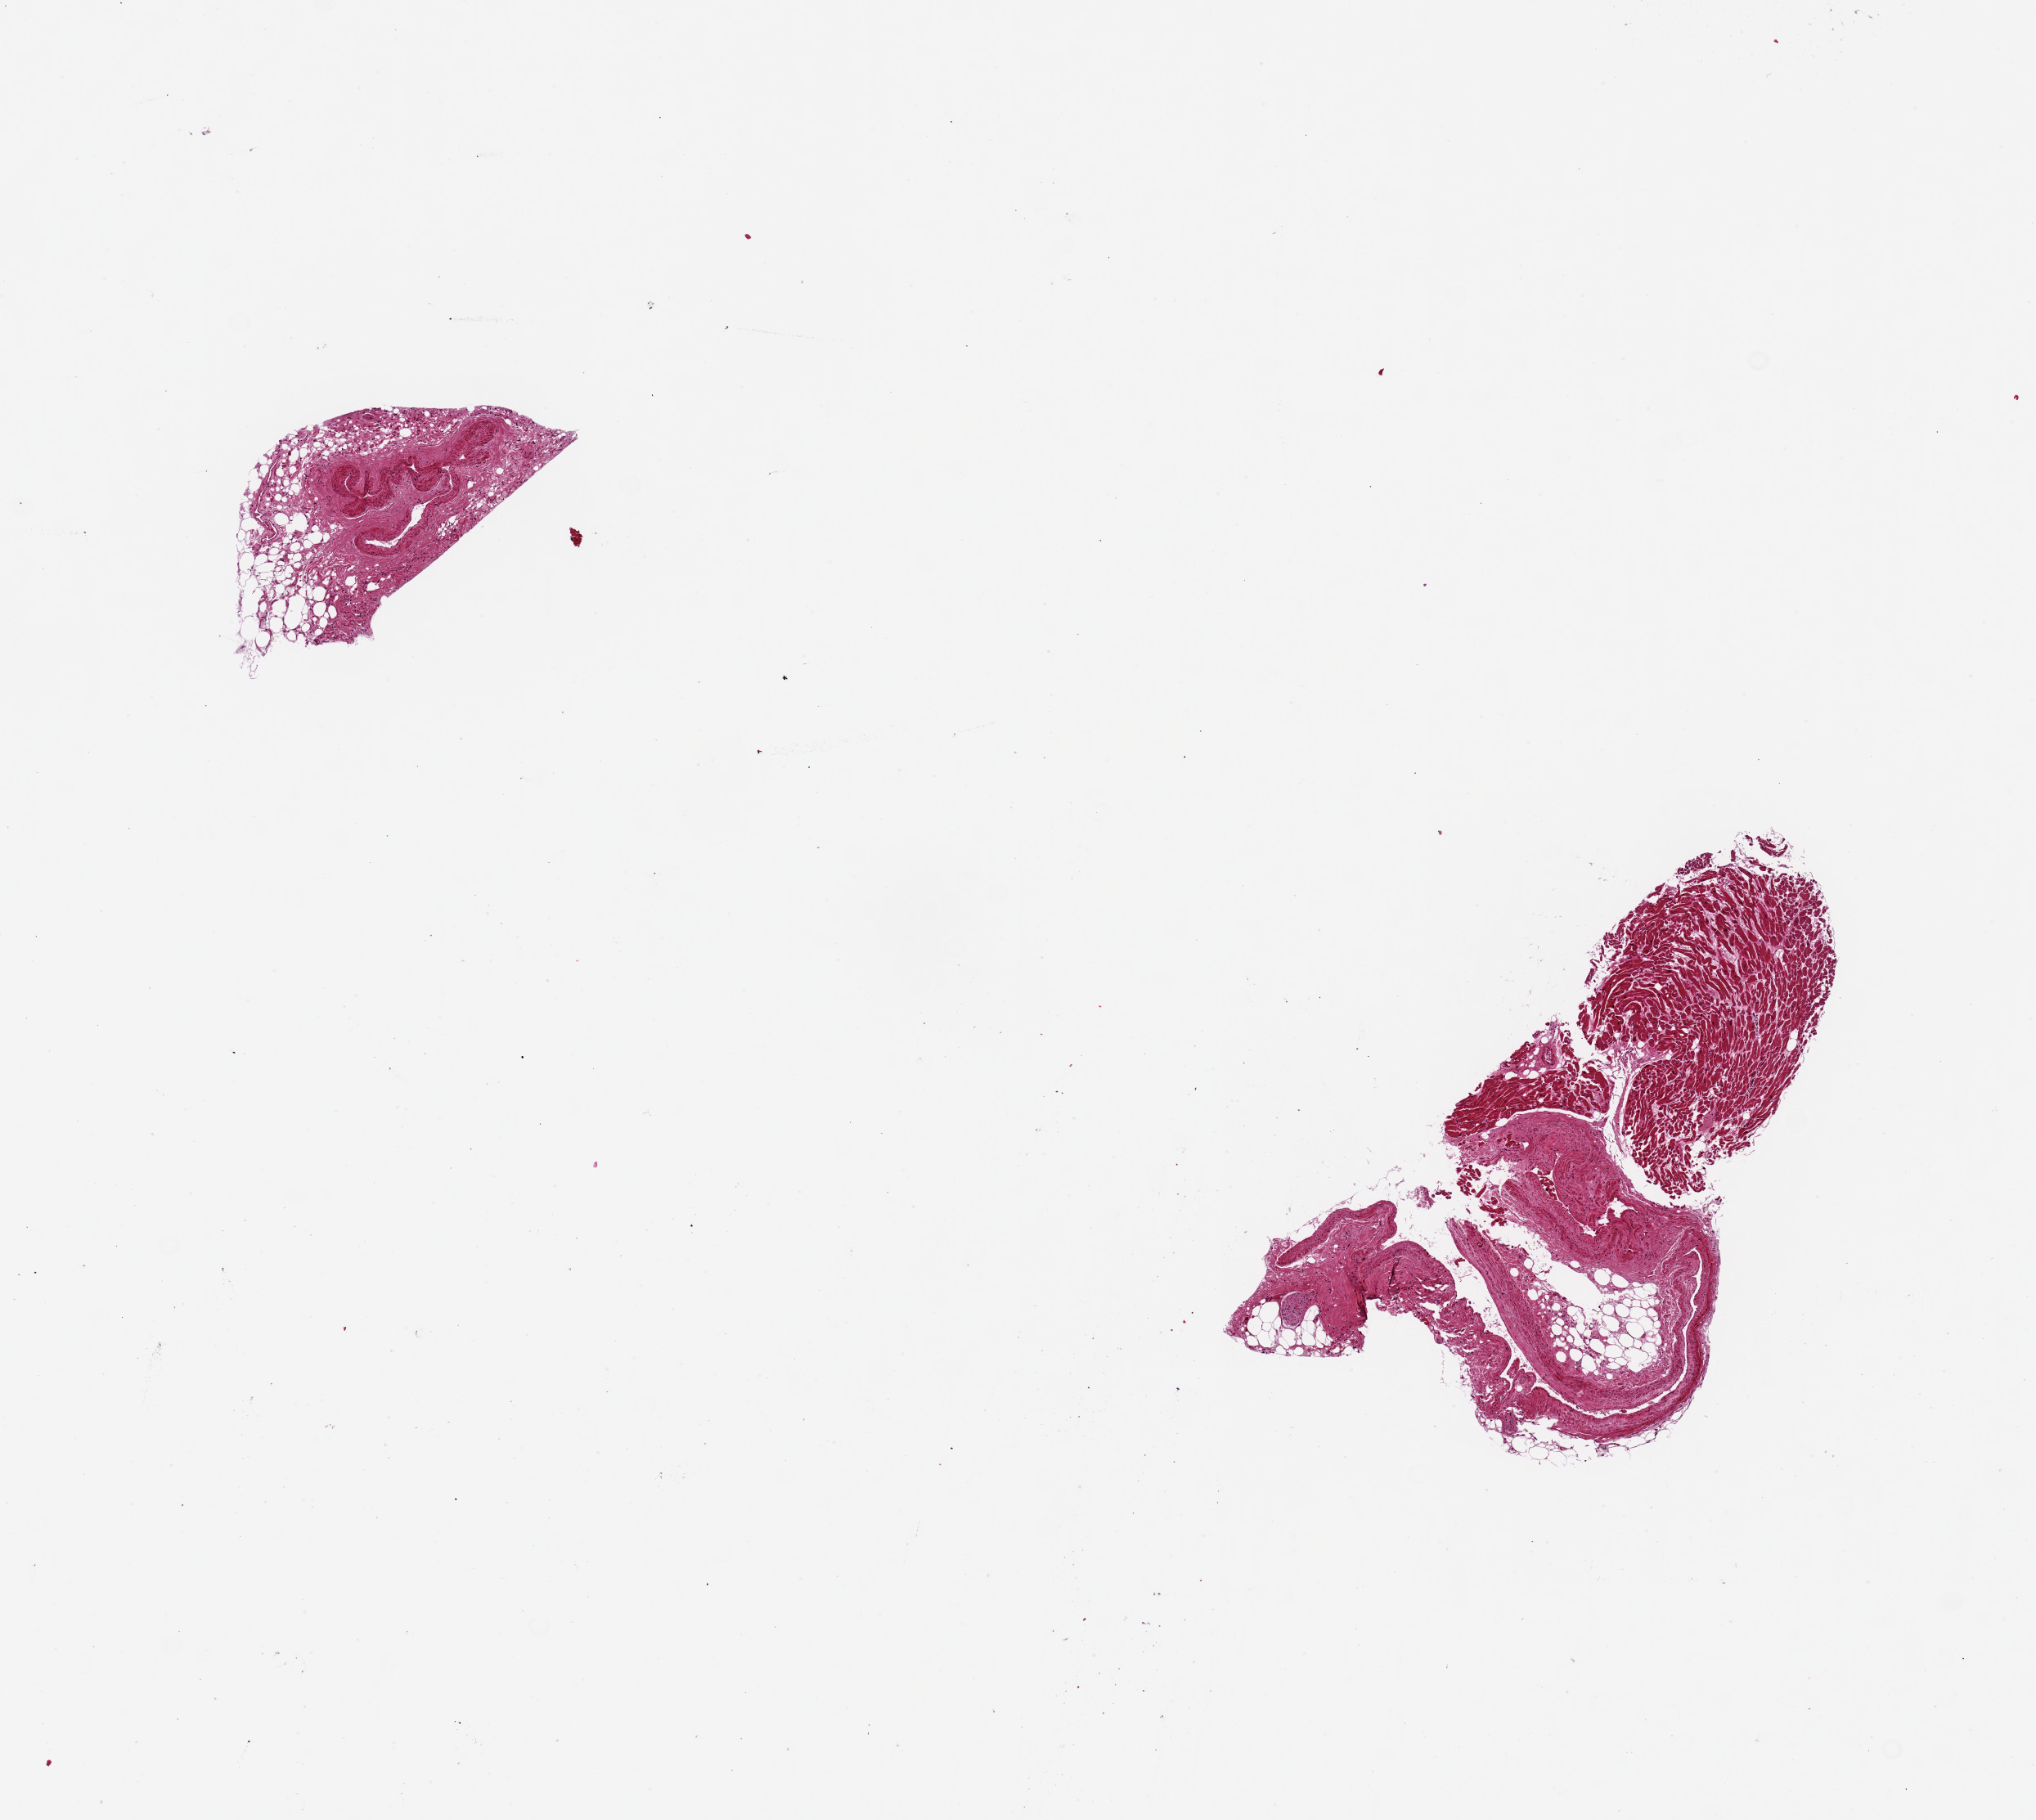
H&E whole-slide image, low-resolution overview of the scanned area, about 9.8 x 8.8 mm; PAXgene-fixed paraffin-embedded (PFPE) section; section of coronary artery (target tissue); tissue donor sample. Donor: female.
• reviewer comment on this tissue sample: 2 pieces, 2mmx982um & 3.5x2mm; up to 1-2mm adherent fat/cardiac muscle; Vessels collapsed